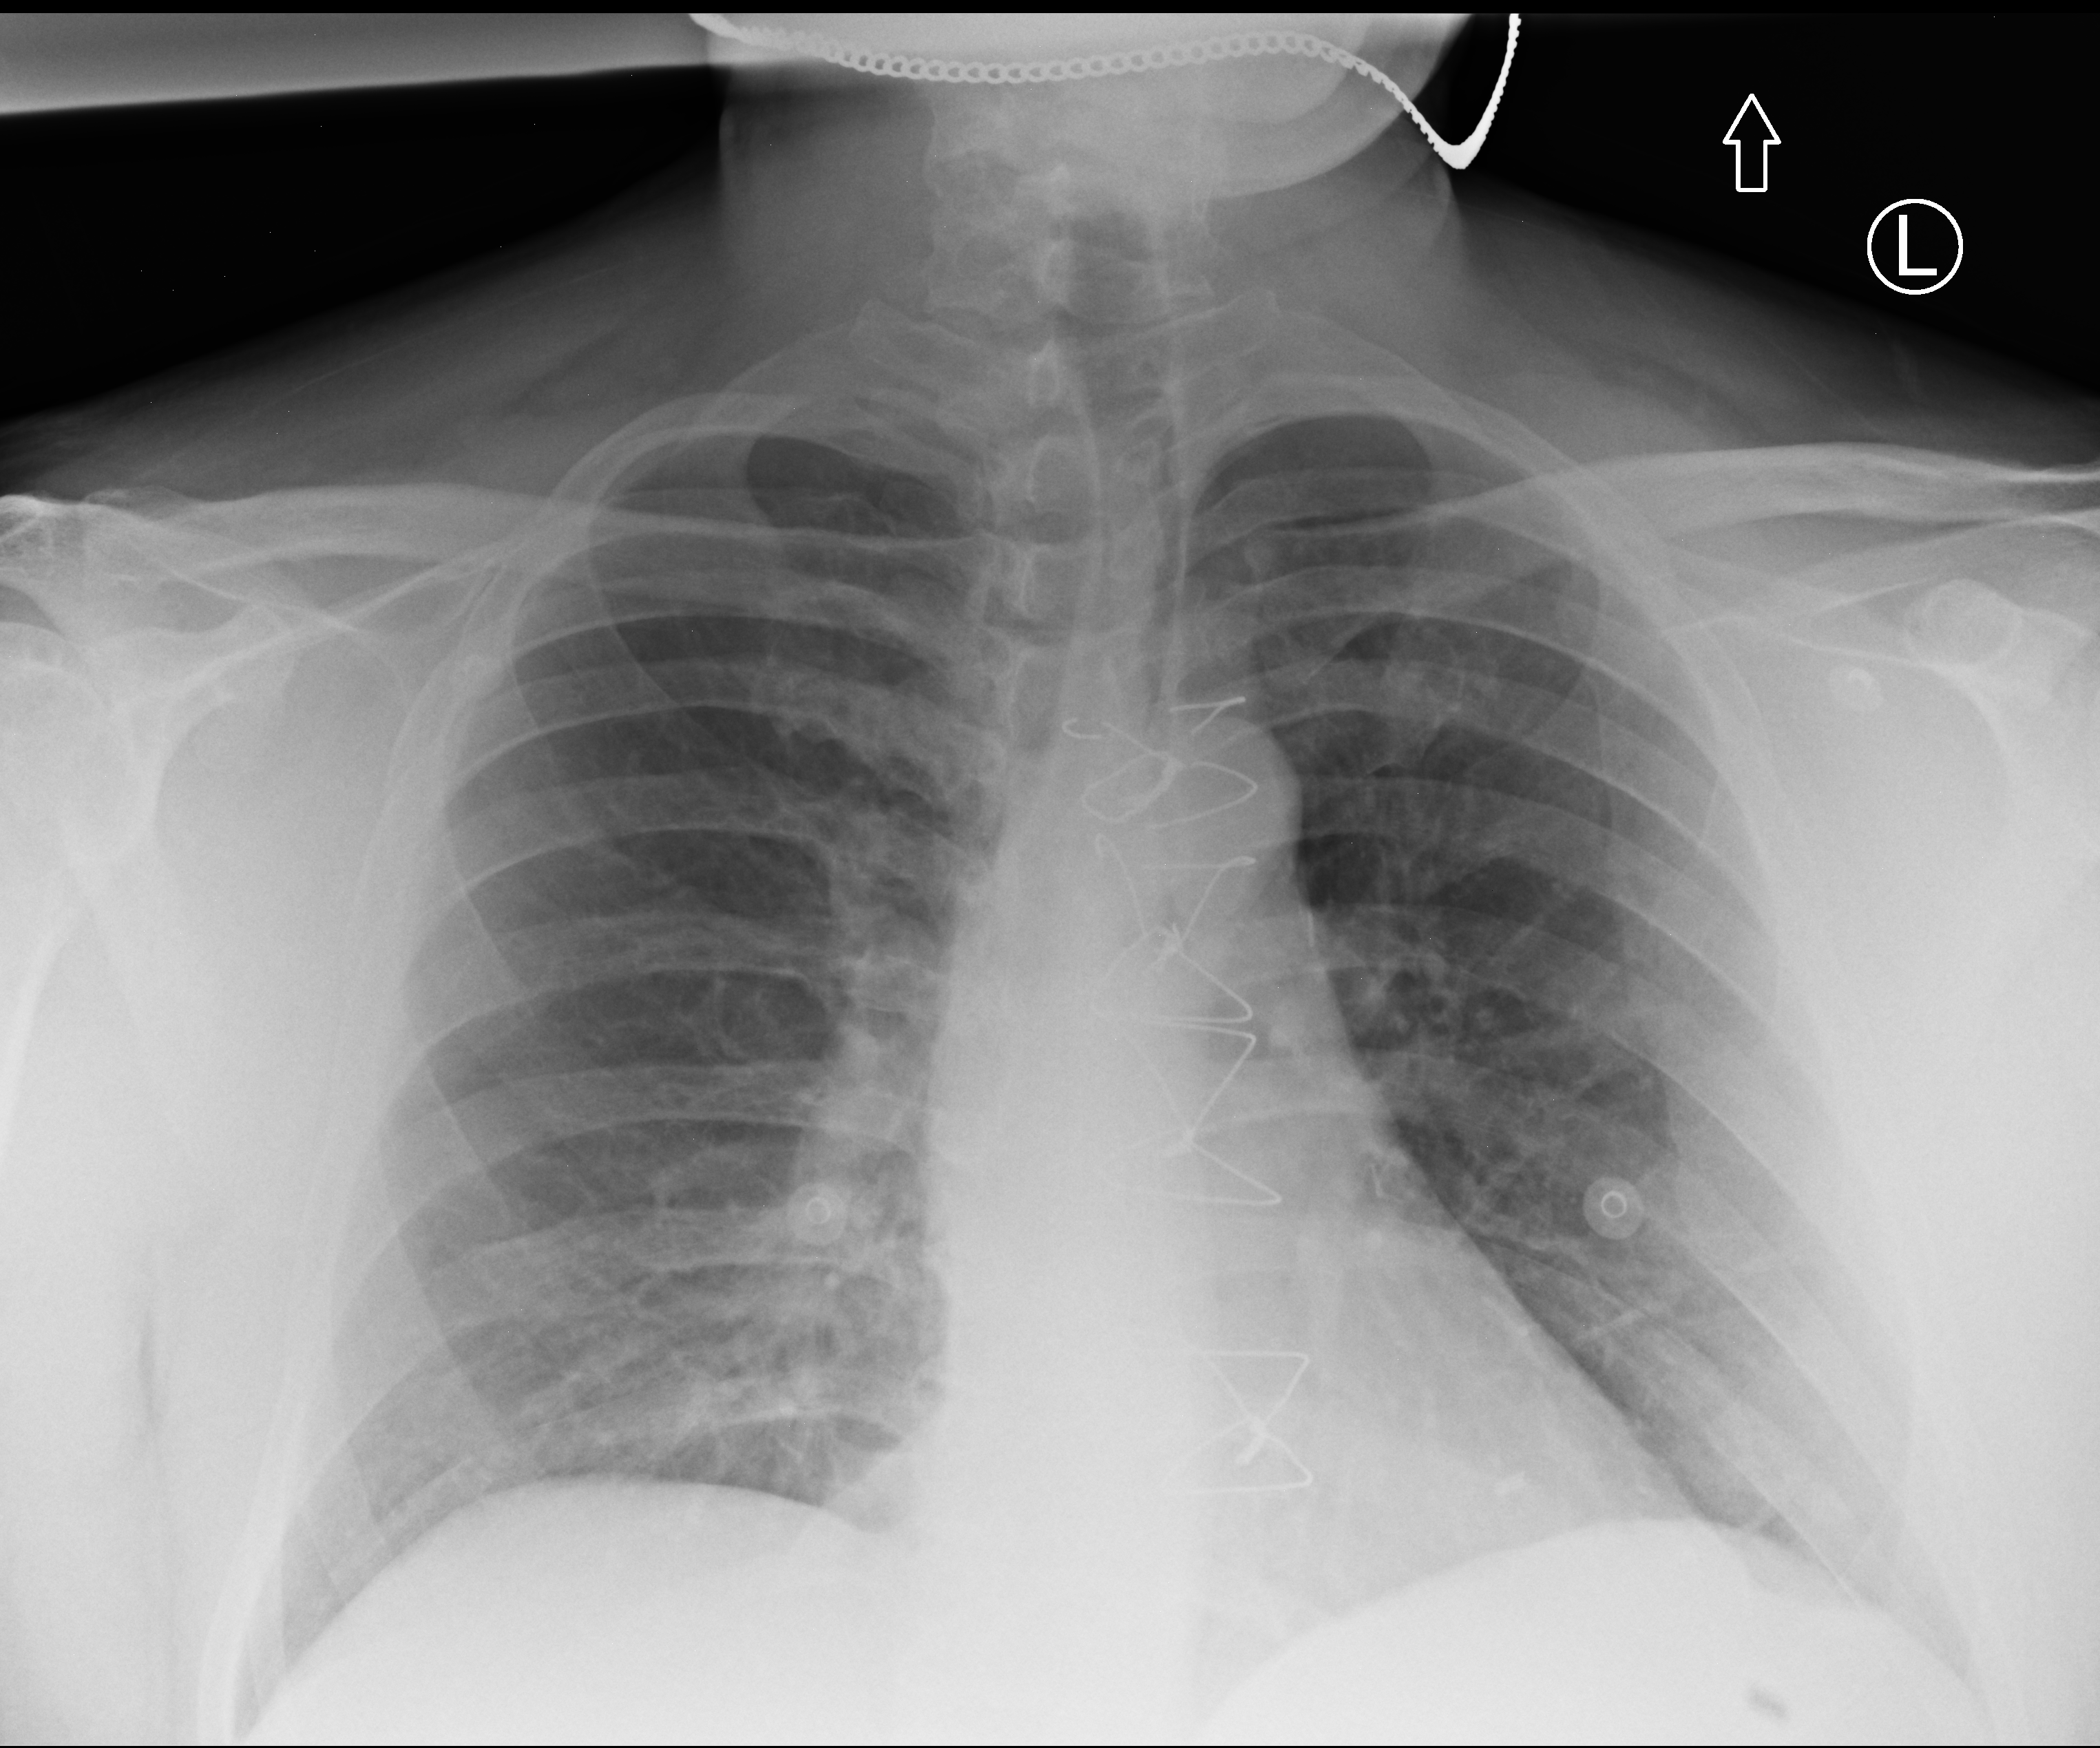
Bedside chest radiograph (computed radiography); anteroposterior (AP) projection. Male patient hospitalised with COVID-19, age 18–59 years.
Hospital-stay facts (about this admission, not read from this image; timing relative to this image not recorded):
- length of hospital stay: 2 days
- mechanically ventilated during this hospital stay: no